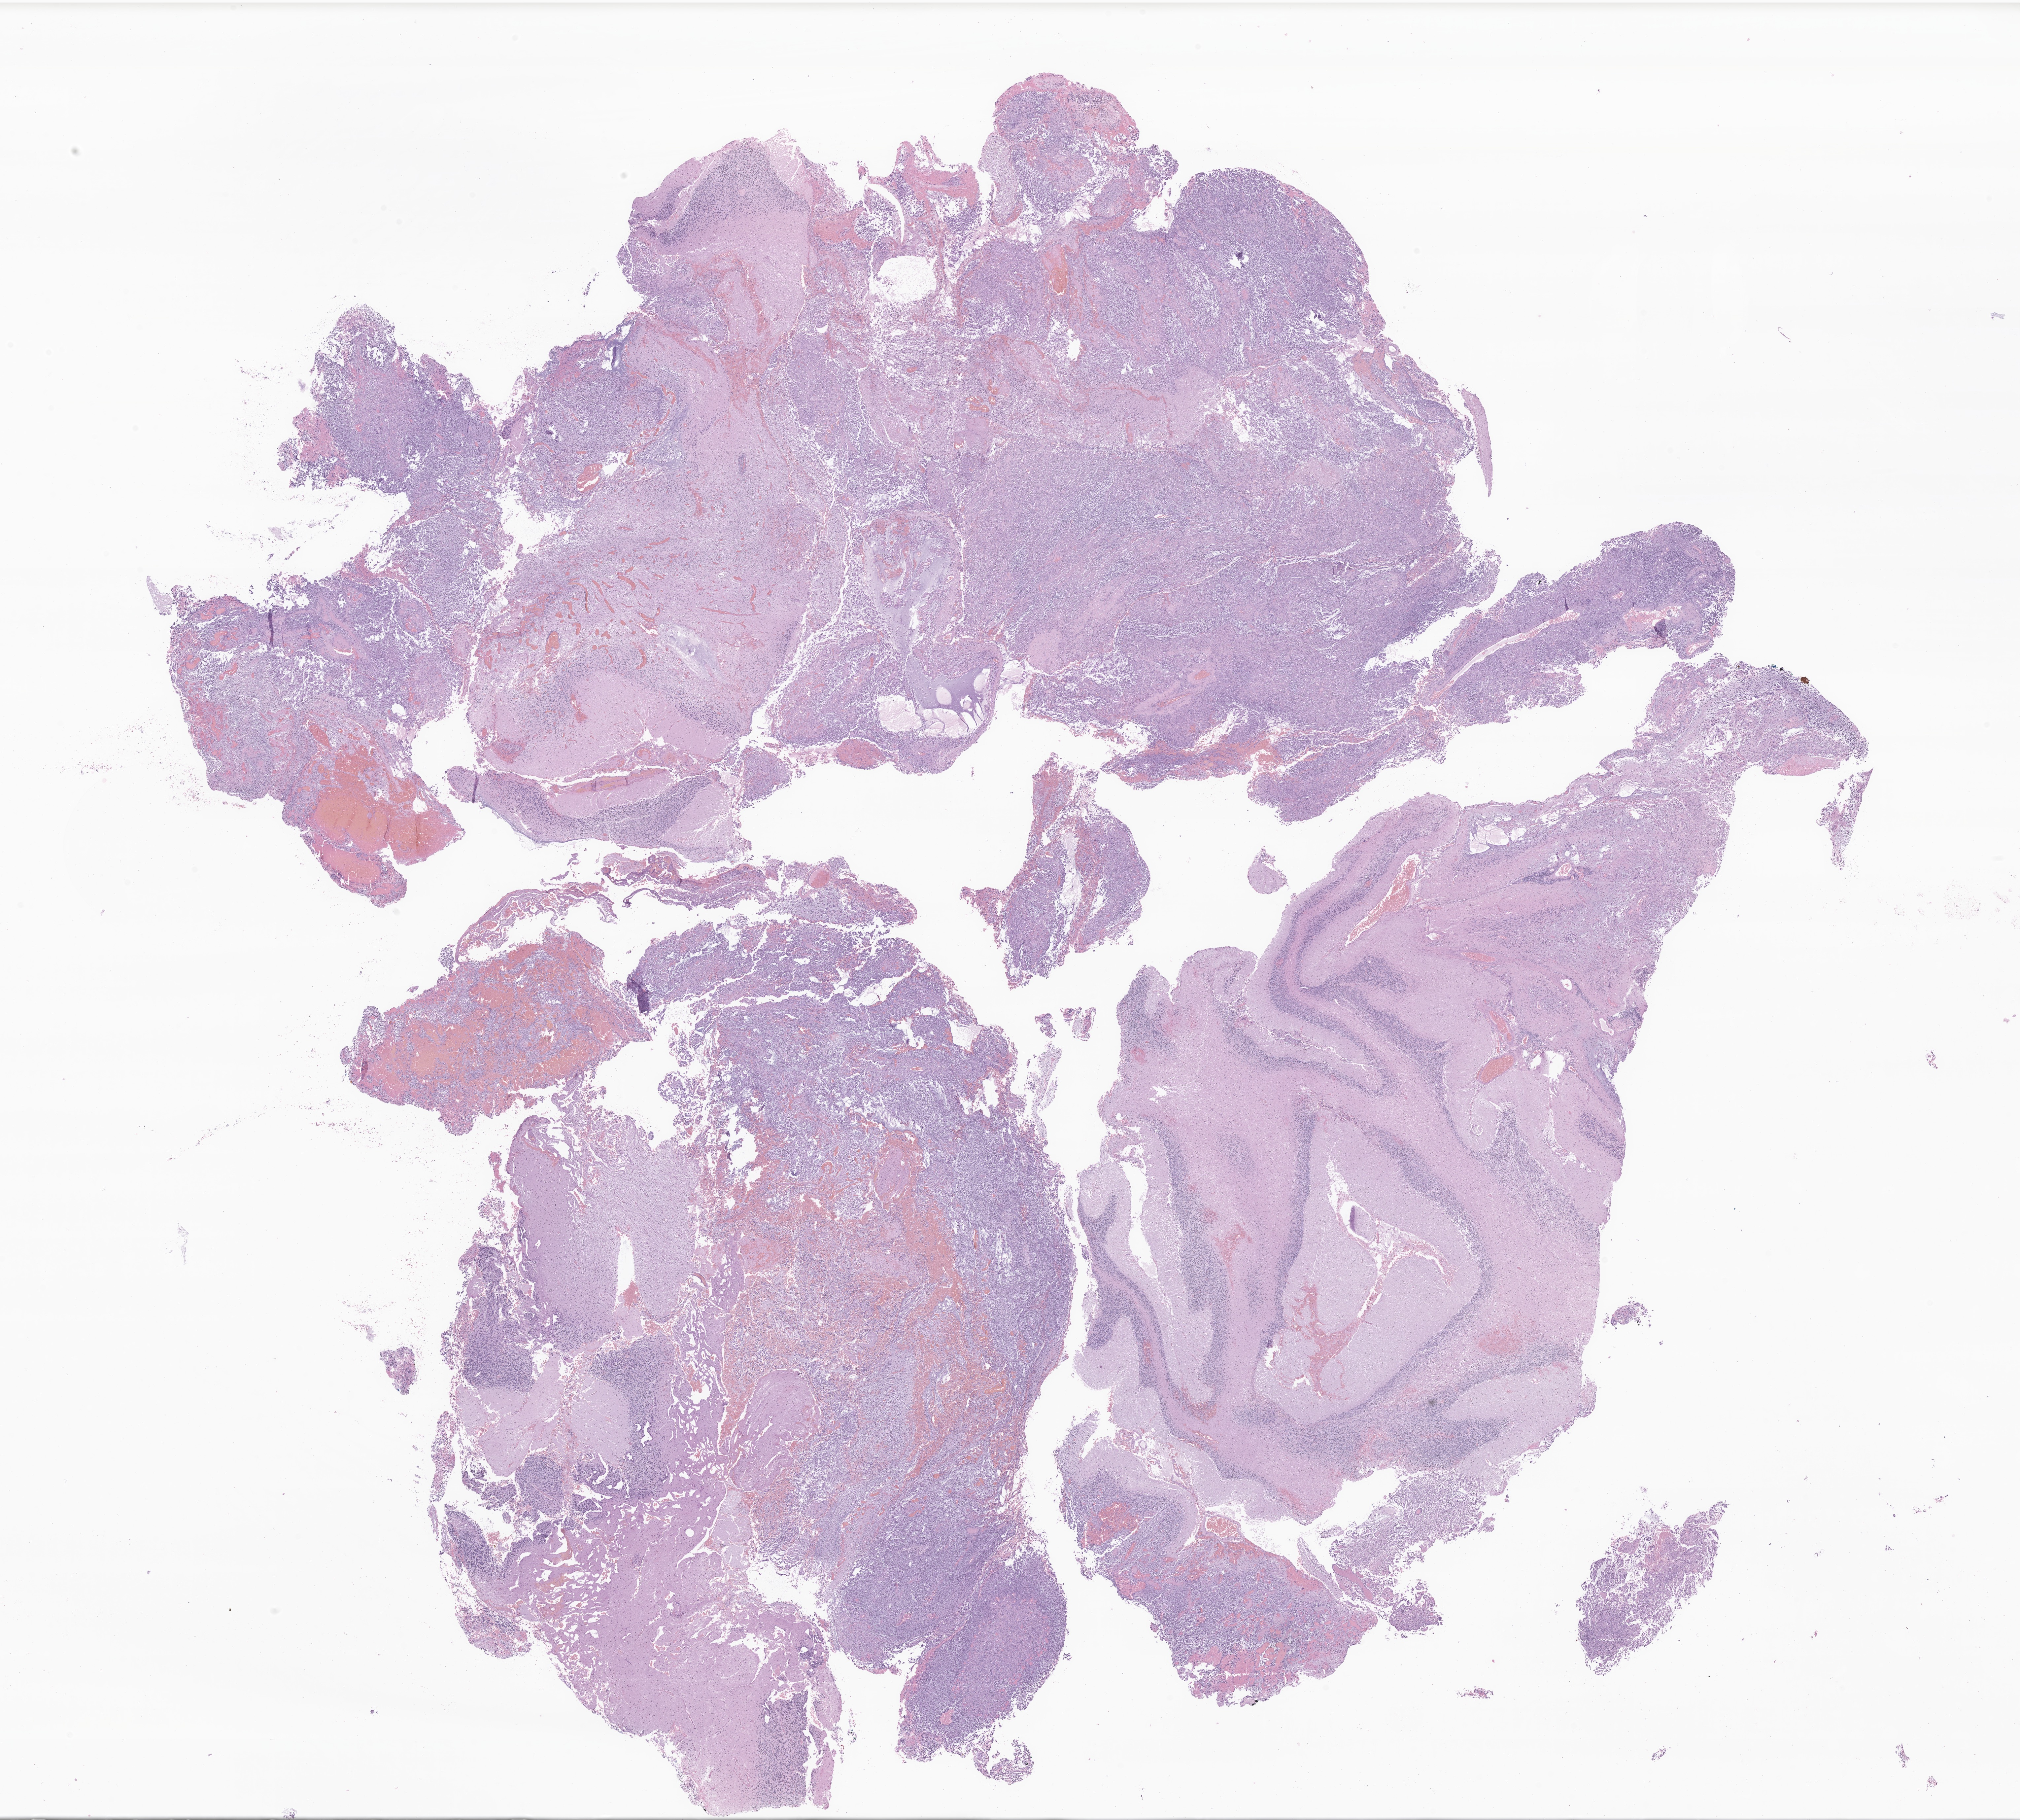
H&E whole-slide image of tumor tissue from the cerebellum — shown as a low-resolution overview of the whole scanned area (about 25.8 x 23.2 mm); formalin-fixed, paraffin-embedded (FFPE) tissue. Female patient, age 252 months (21 years).
• diagnosis: Glioma, malignant